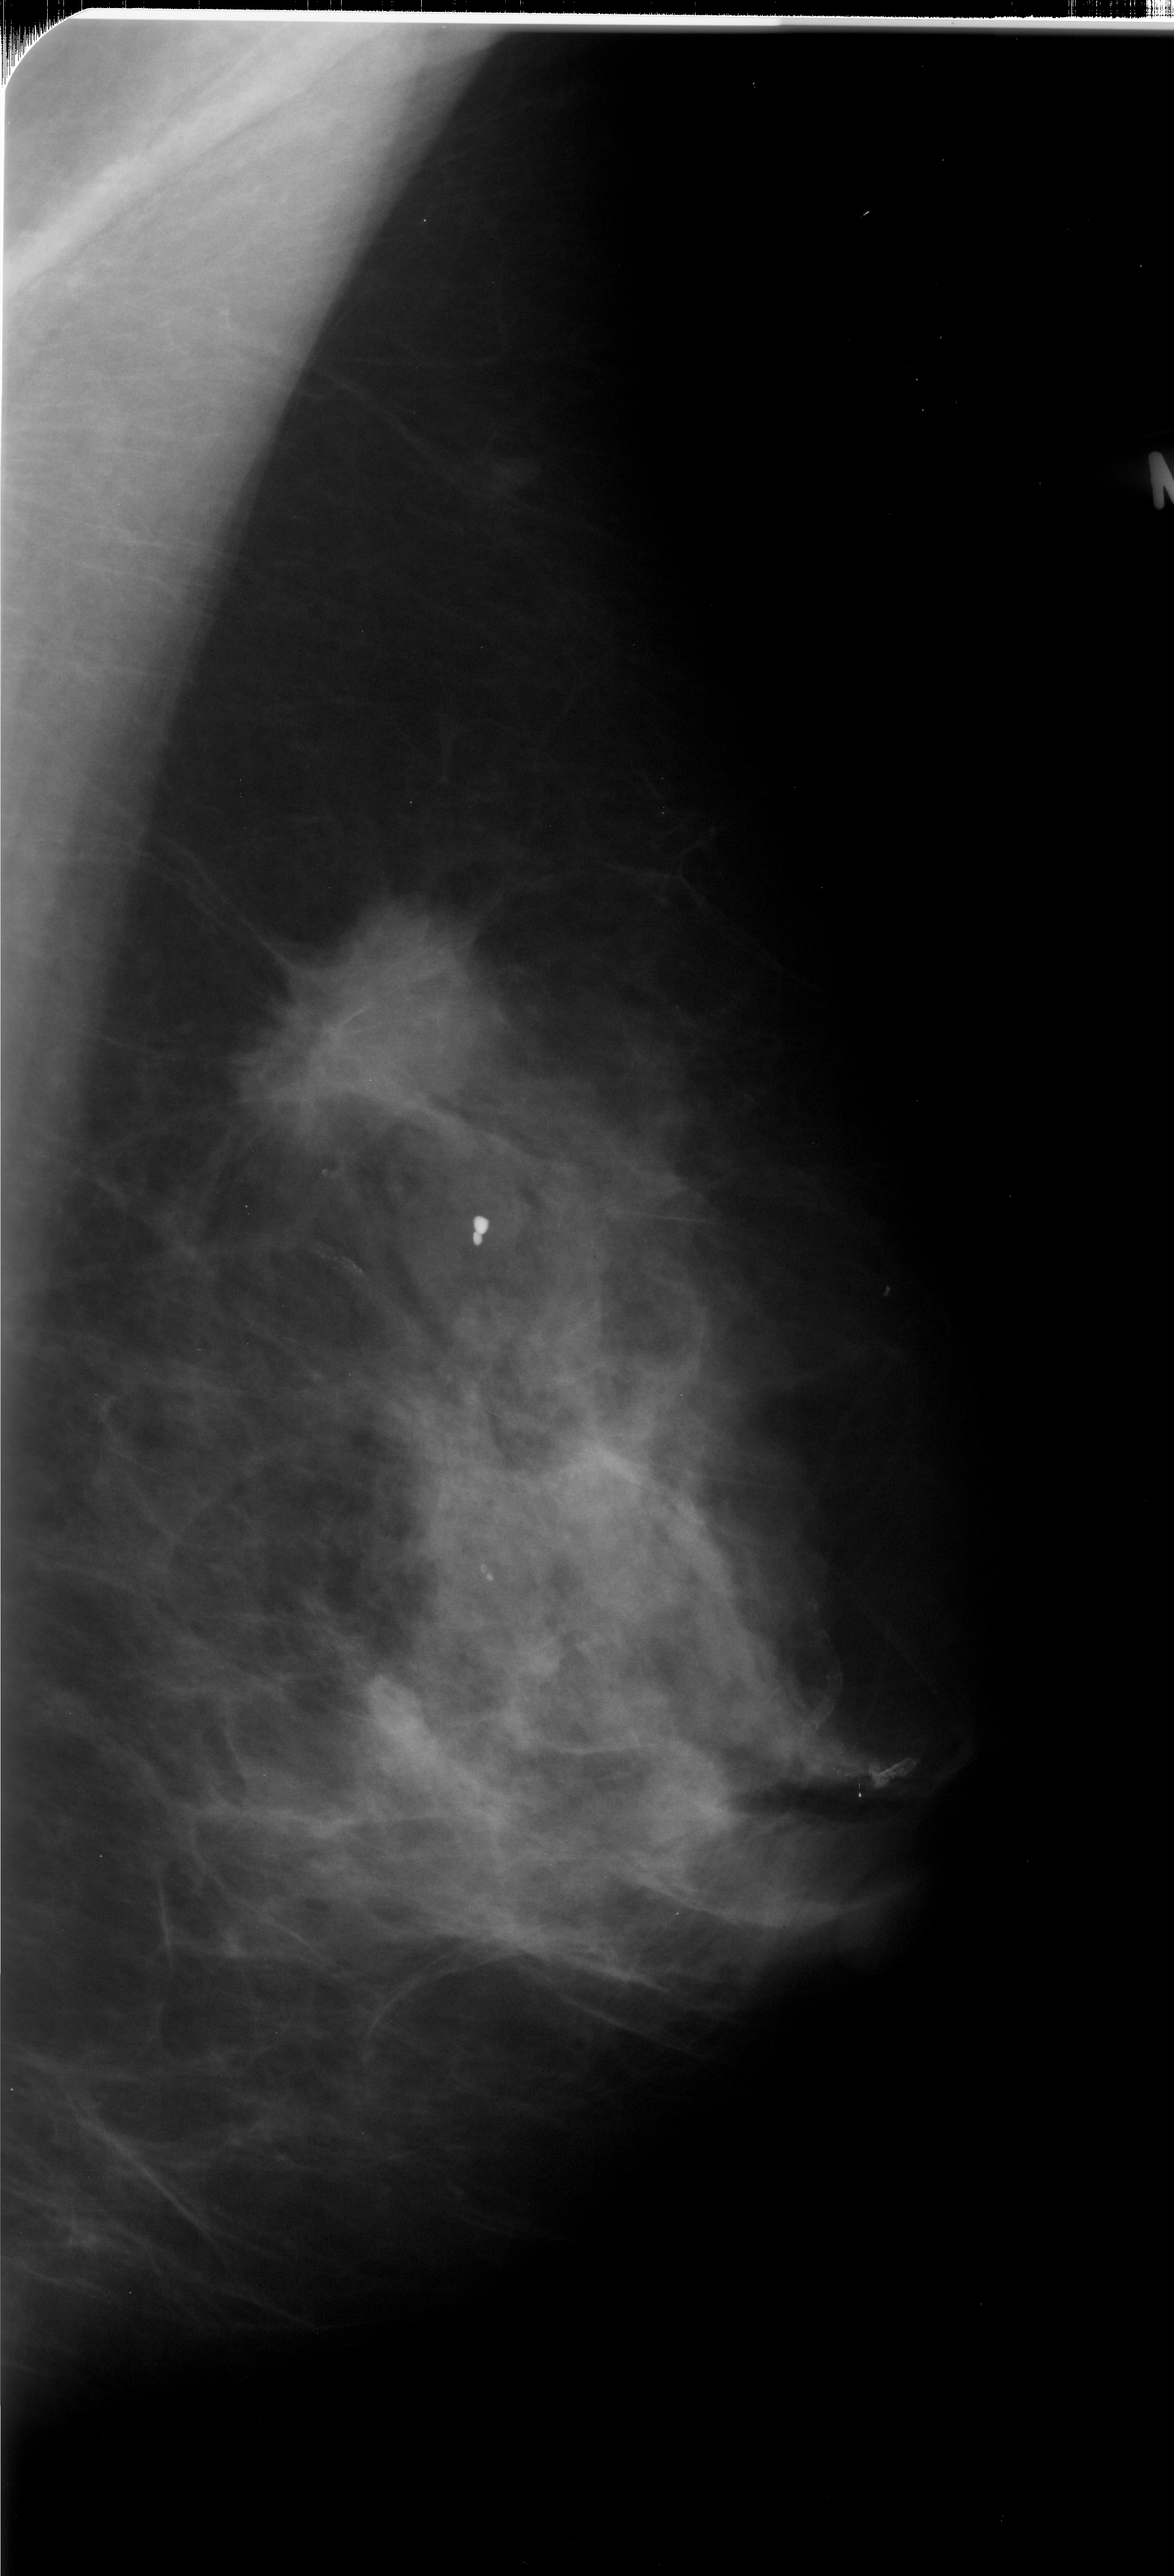
Mammogram (digitized film). Right breast. Mediolateral oblique (MLO) view. BI-RADS breast density category 3 (scale 1–4). 1174 × 2576 image matrix.
Expert-marked regions of interest on this image (one box per marked abnormality):
- mass, shape irregular, margins spiculated; BI-RADS assessment category 5; subtlety rating 5 on a 1 (subtle) to 5 (obvious) scale; pathology (as recorded): malignant: bounding box <250,904,492,1137> (left, top, right, bottom; pixels)